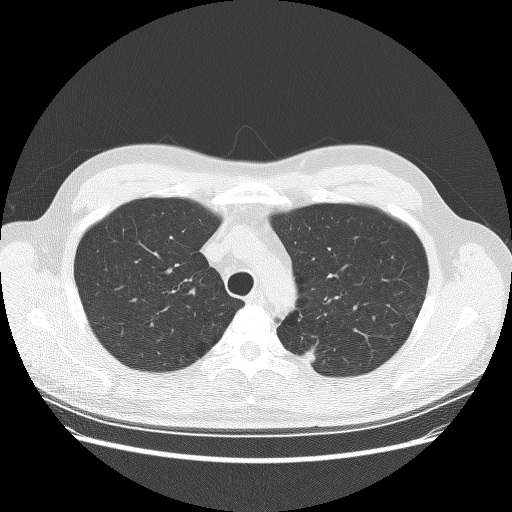
Low-dose screening chest CT, one axial slice. Slice 204 of 253 in the series (ordered by position). Reconstruction kernel BONE. 120 kVp. Lung window (W 1500 / L -600 HU). 2.5 mm slice thickness. 512 × 512 image matrix.
Outlined on this slice (manually delineated by an expert):
- lesion 2 (nodule): bounding box [x1, y1, x2, y2] px = [305, 348, 316, 363]